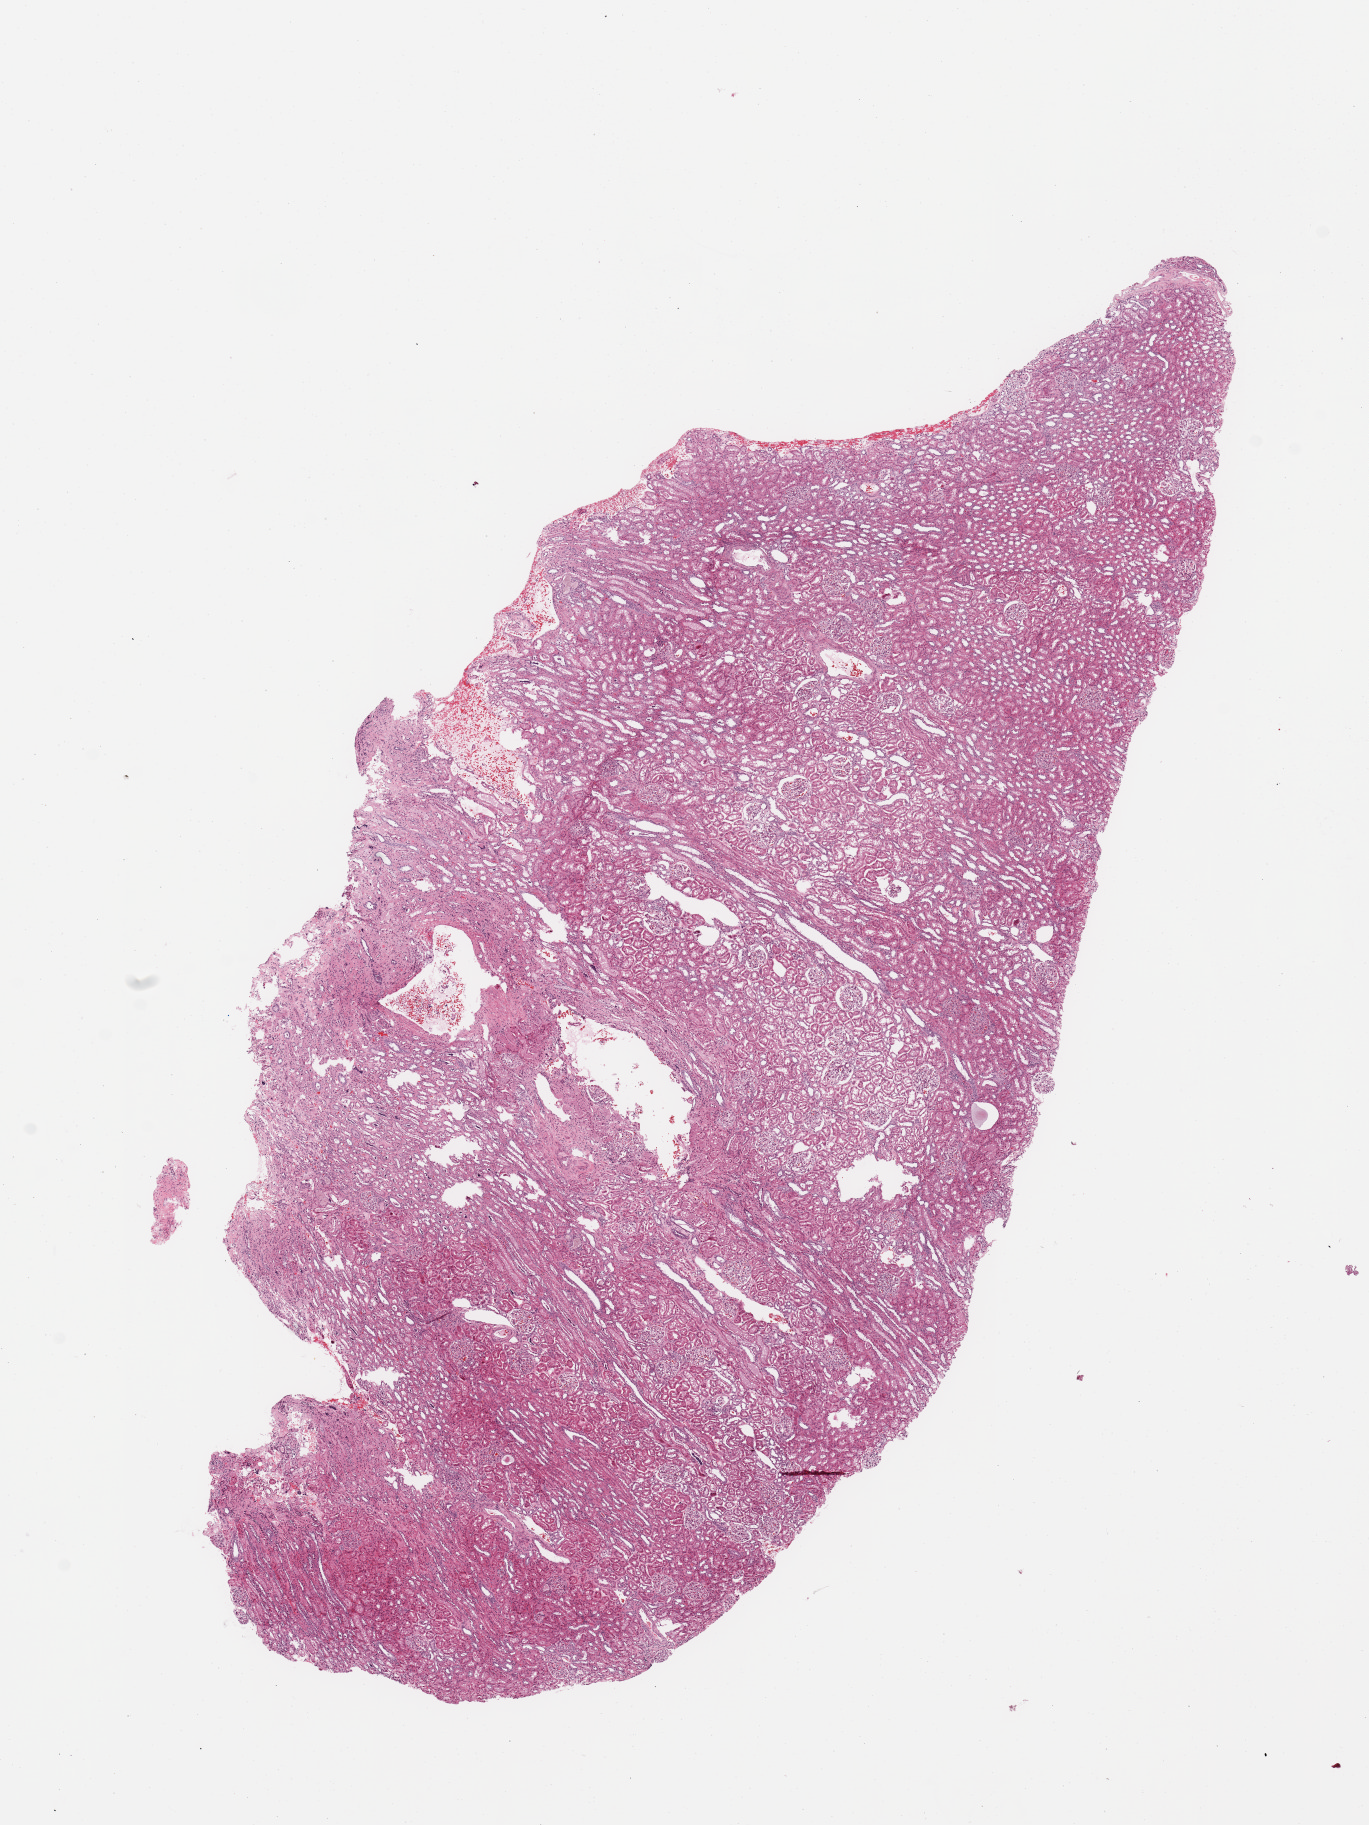
H&E-stained whole-slide image, a low-resolution overview of the entire scanned area, about 10.8 x 14.4 mm (acquisition: 20x scan). Normal (non-tumour) tissue sample. Female, 54 y/o.
- this section: normal (non-tumour) tissue from the same patient
- patient diagnosis (cohort enrolment): sarcoma (site not recorded at cohort level)